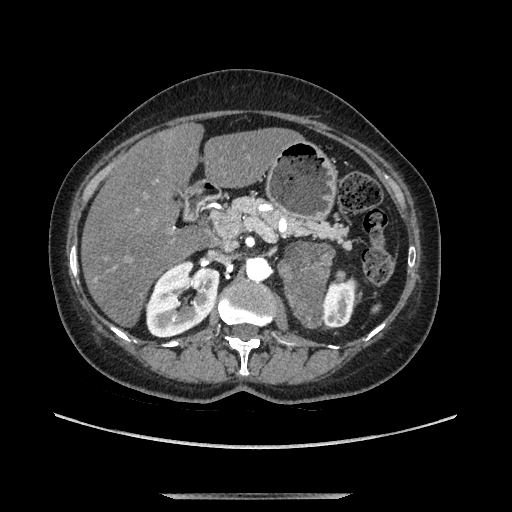
Contrast-enhanced abdominal CT, one axial slice. Position 65 of 169 along the scan axis. Soft-tissue window (W 400 / L 40 HU). 1.25 mm slice thickness. 512 × 512 image matrix, field of view 400 × 400 mm. Female patient. From the clinical record (not read from this slice): diagnosis: adrenocortical carcinoma; tumour side: left adrenal; tumour size at pathology: 9 cm; Ki-67 index: 2 %; stage (as recorded): 3.
Annotated regions visible in this slice (semi-automatically segmented with operator editing):
- mass: box from (x=283, y=244) to (x=333, y=328) px